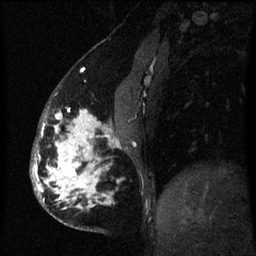
Breast MRI (dynamic contrast-enhanced), one sagittal slice; position 22 of 60 along the scan axis; dynamic contrast-enhanced series, image 2 of 3 at this slice position (ordered by acquisition); 1.5 T; TE 4.2 ms, TR 8 ms; 256 × 256 image matrix. Female patient, age 50 years.
Structures marked on this image (semi-automatically segmented with operator editing):
- analysis volume of interest (the breast-tissue region the enhancement analysis was run in; not a lesion): box from (x=32, y=107) to (x=118, y=231) px
- tumour enhancement mask (voxels above the 70 % enhancement threshold inside the analysis volume of interest): (x=32, y=110)–(x=100, y=209)